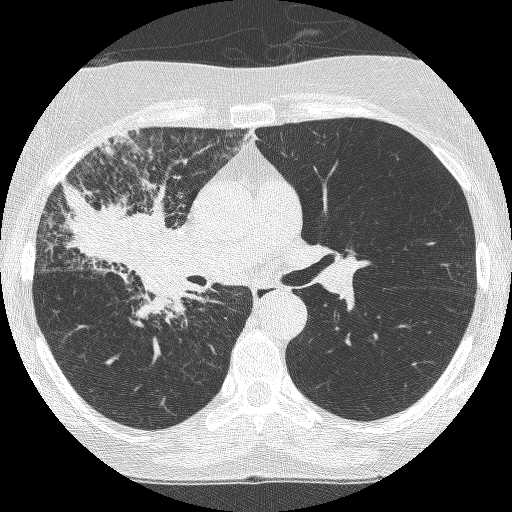
Axial slice from a low-dose chest CT screening exam; third annual screen; lung window (W 1500 / L -600 HU); 120 kVp; 512 × 512 image matrix, field of view 294 × 294 mm. Female participant, aged 64 years at enrolment.
Expert reader's lesion annotation, bounding box [x1, y1, x2, y2] px = [70, 186, 202, 320]. Reader record for this screening exam (exam-level; its link to the box is not recorded): non-calcified nodule or mass ≥4 mm, right upper lobe, 49 × 43 mm, spiculated (stellate) margins, soft tissue attenuation, pre-existing on the prior screen: yes; interval growth: yes. Official screen result: positive, other.